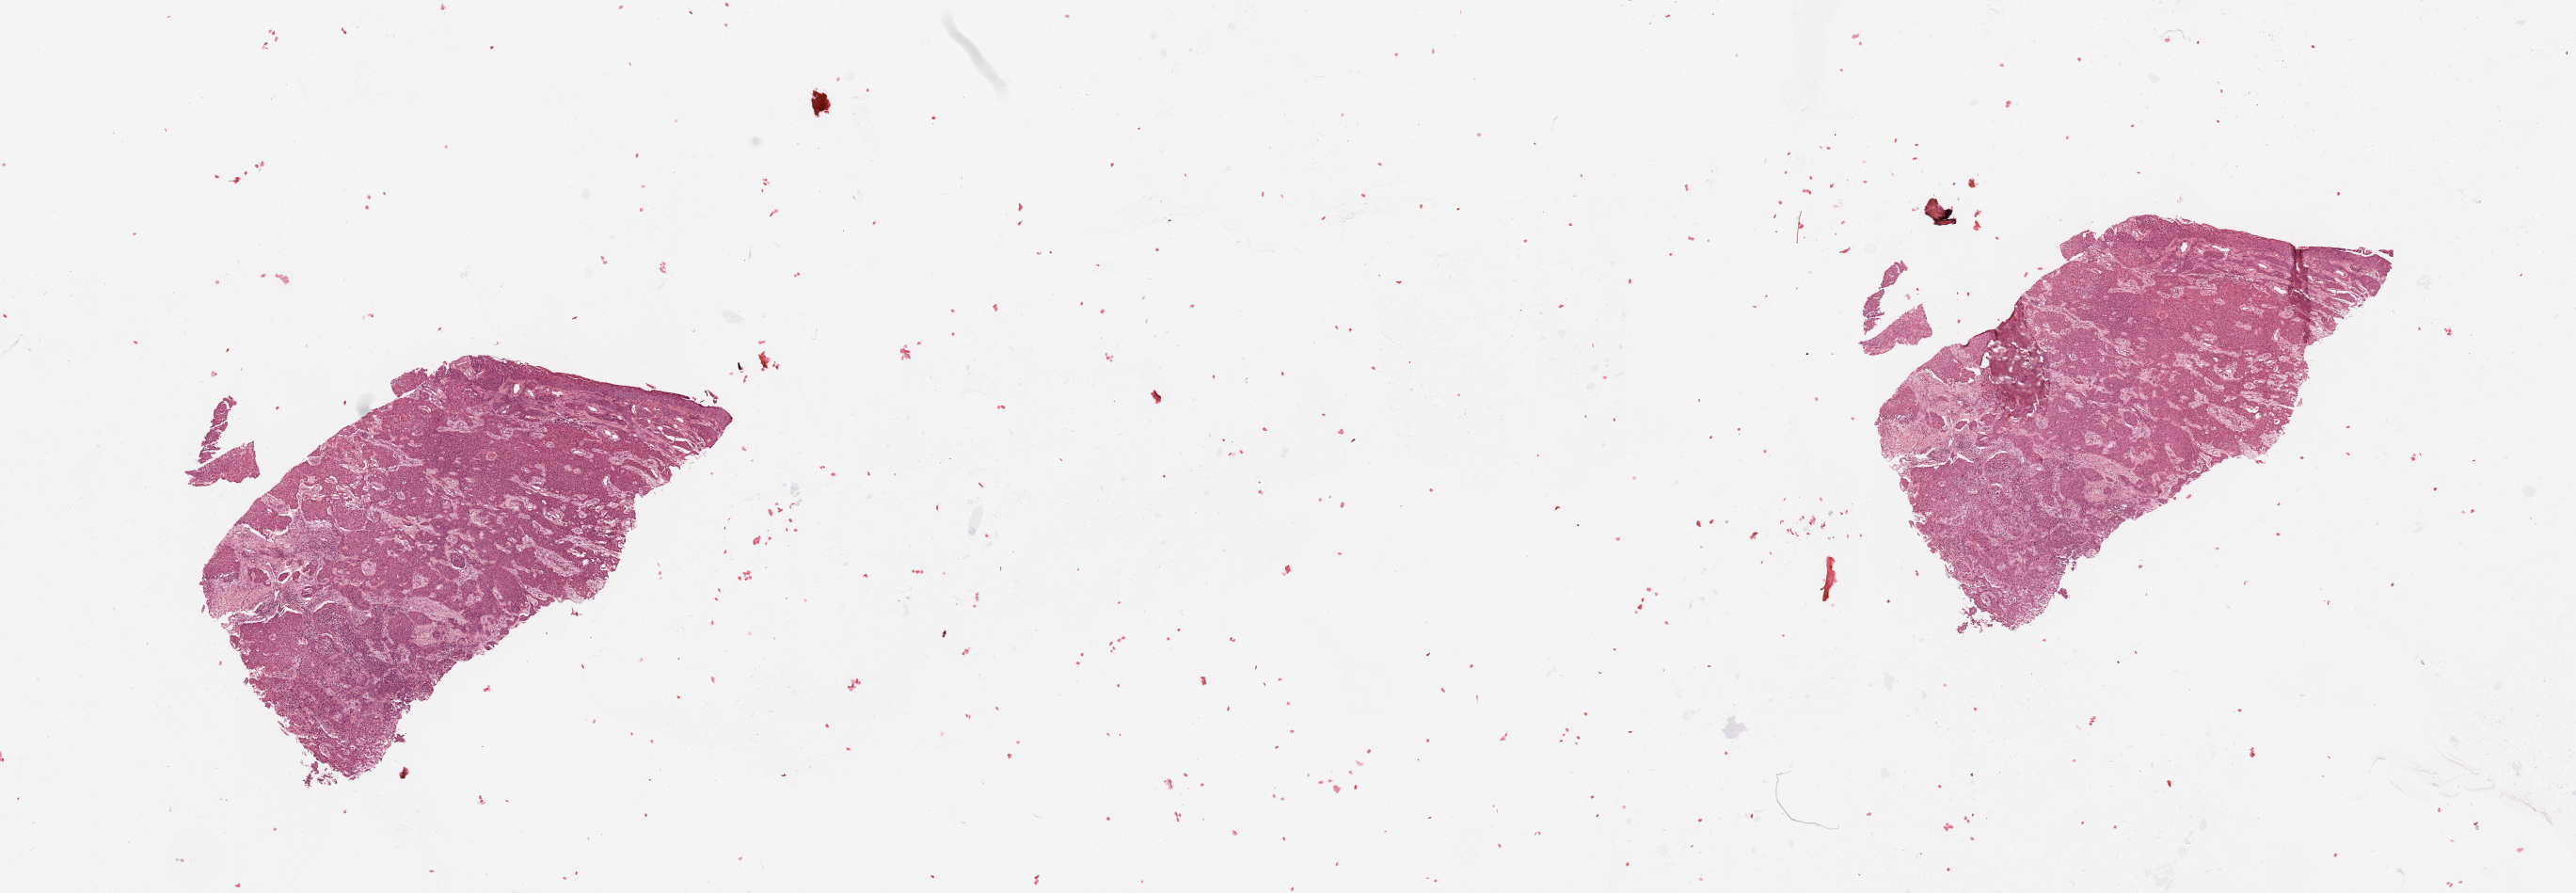
Whole-slide histology image, H&E-stained, low-resolution overview of the scanned area, about 21.7 x 7.5 mm; head and neck, tissue type not recorded. Female, 53 y/o.
• patient diagnosis: Squamous cell carcinoma, NOS (larynx, NOS)